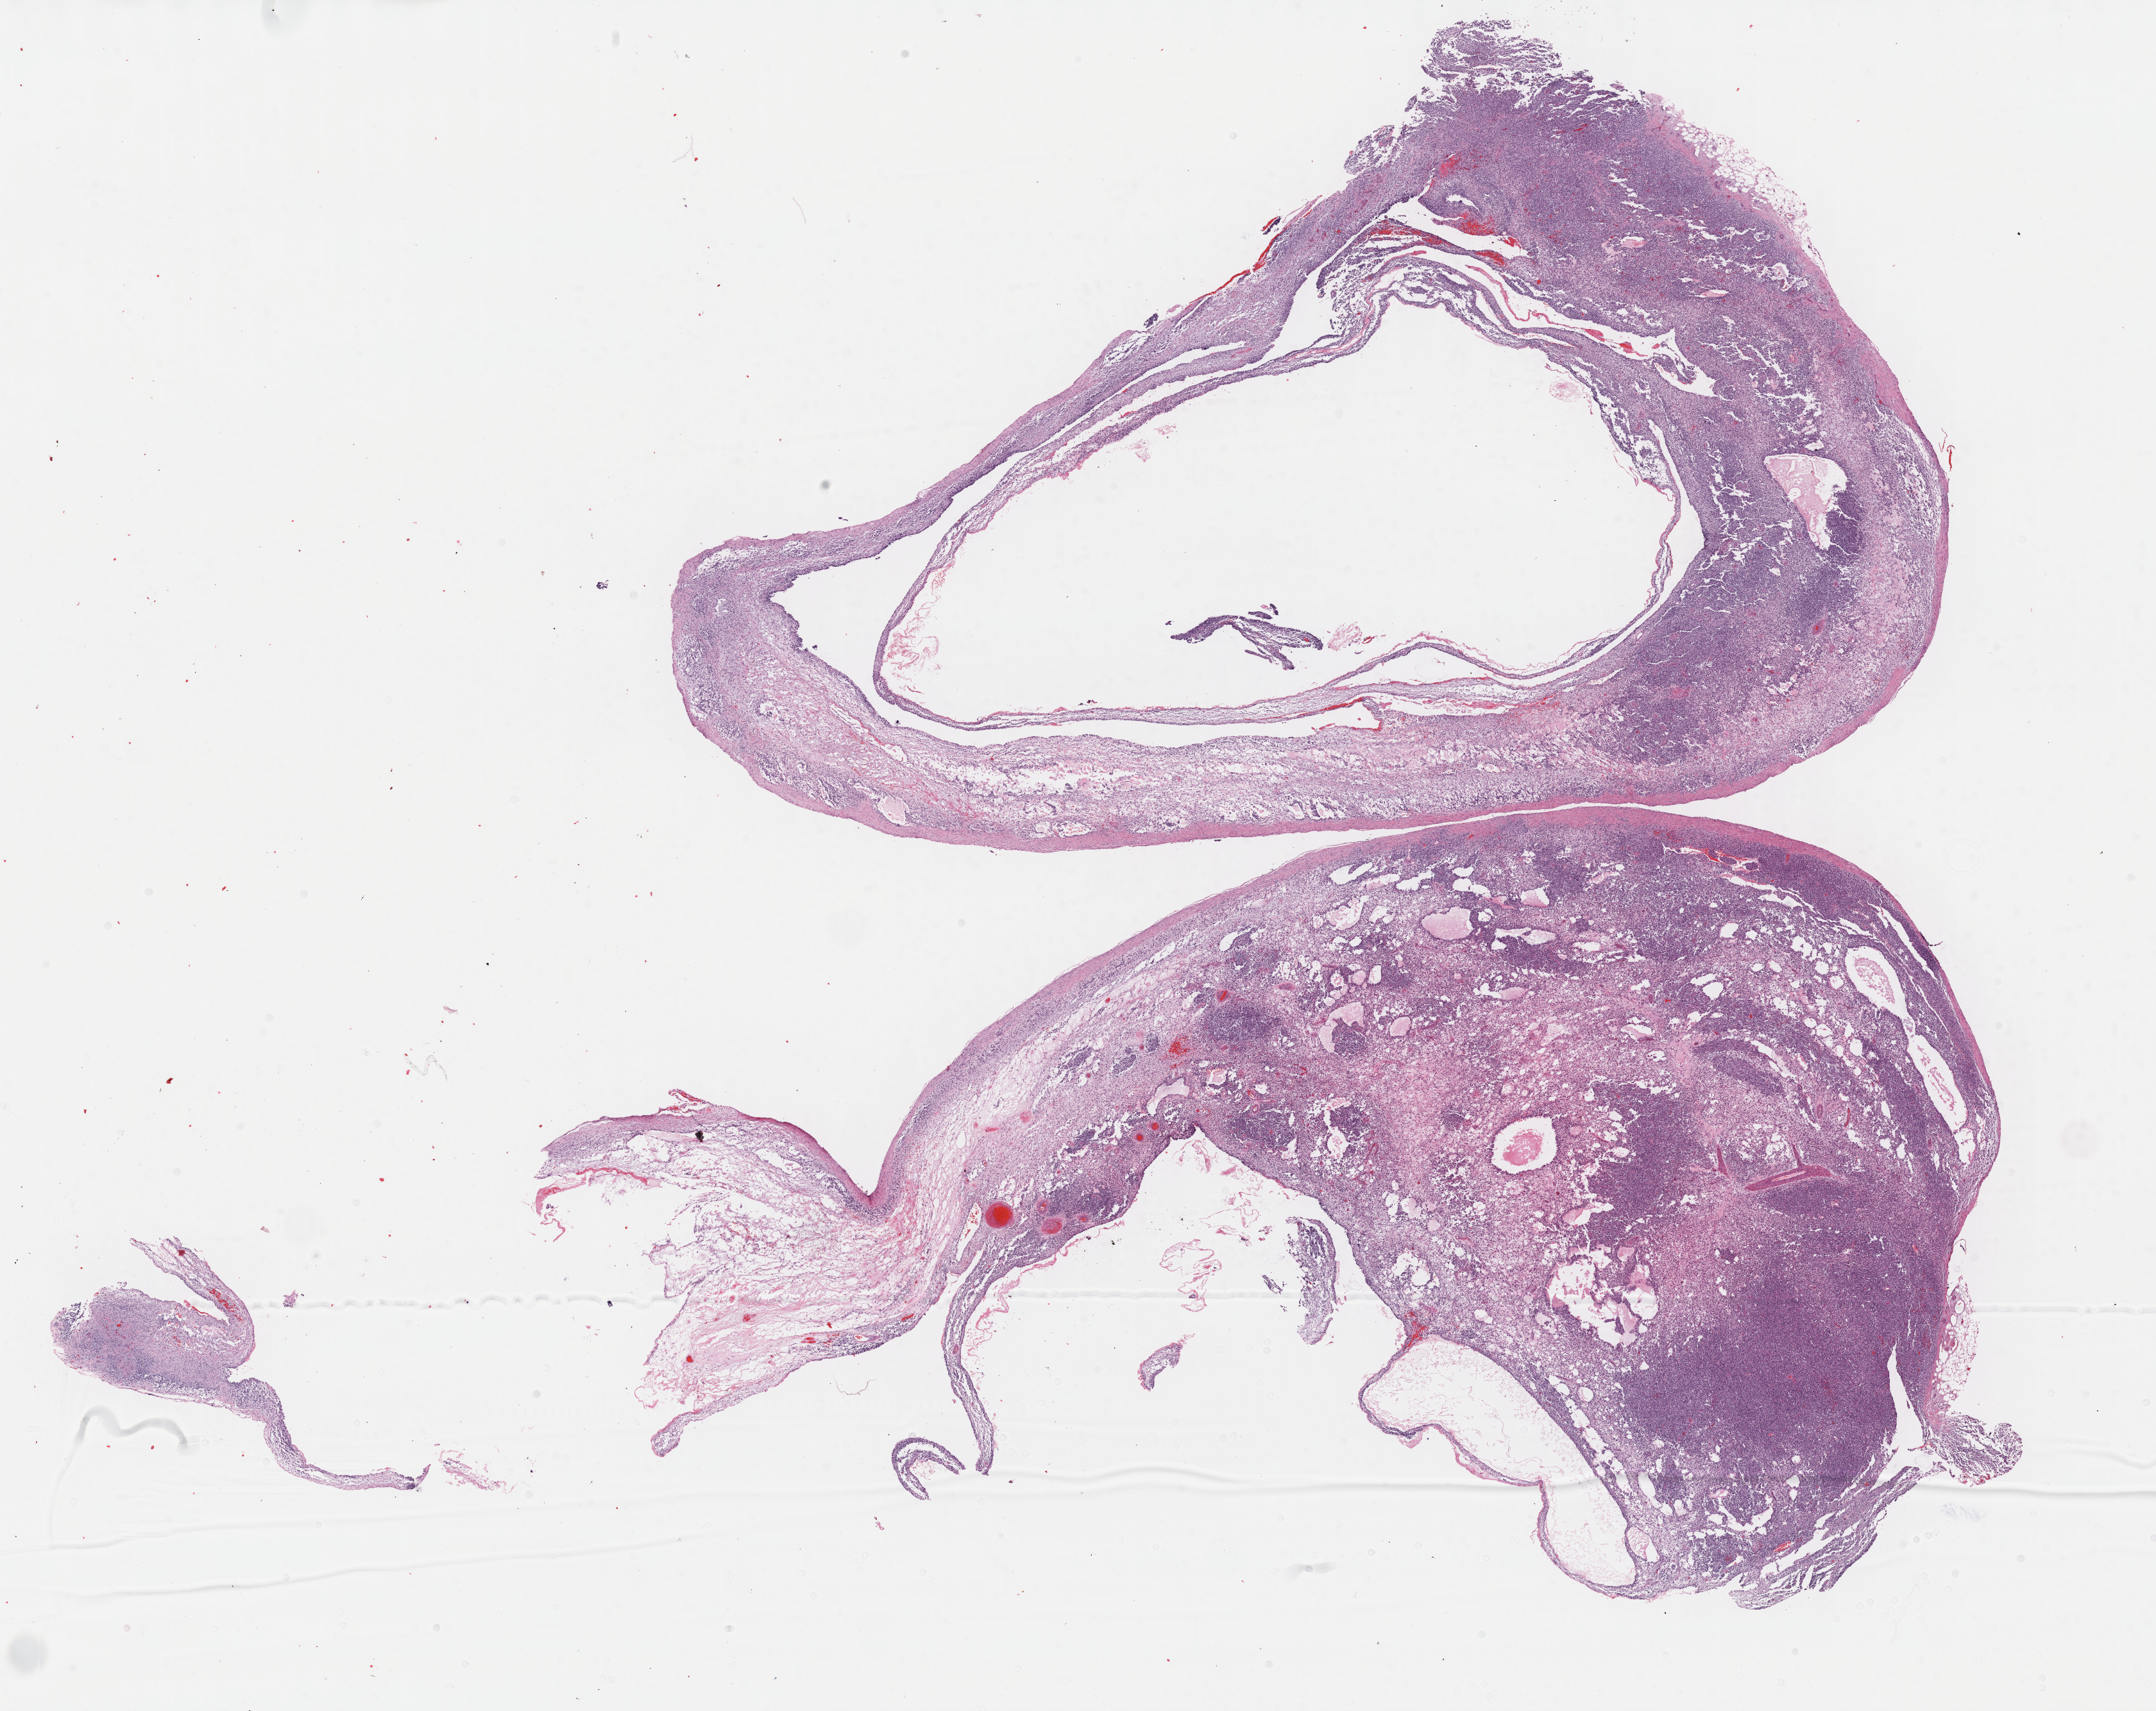
Digitized H&E-stained tissue section (whole slide), low-resolution overview of the scanned area, about 27.2 x 21.6 mm, formalin-fixed paraffin-embedded (FFPE) diagnostic section, primary tumour sample from the retroperitoneum and peritoneum. Male patient; age at initial diagnosis 57 years.
Pathologic diagnosis: Dedifferentiated liposarcoma (retroperitoneum).